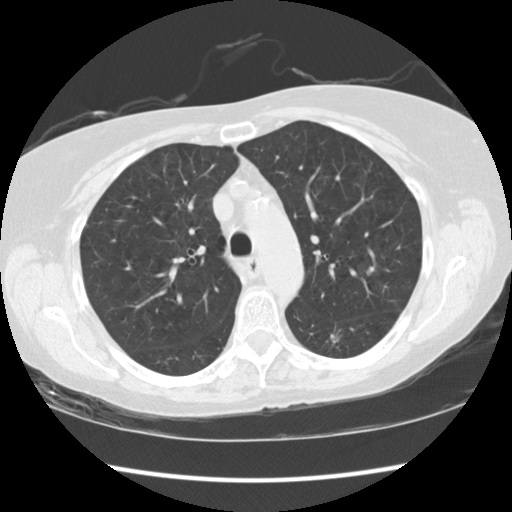
Low-dose screening chest CT, one axial slice. Position 85 of 119 along the scan axis. Reconstruction kernel STANDARD. Lung window (W 1500 / L -600 HU). 2.5 mm slice thickness. 512 × 512 image matrix, field of view 334 × 334 mm.
Annotated regions visible in this slice (outlined manually by an expert reader):
- lesion 1 (tumor, lower lobe of left lung): box from (x=330, y=334) to (x=338, y=343) px